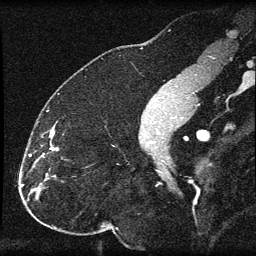
Breast MRI (dynamic contrast-enhanced), one sagittal slice. Dynamic contrast-enhanced series, image 2 of 3 at this slice position (ordered by acquisition). 1.5 T. TE 4.2 ms, TR 8.2 ms. 2 mm slice thickness. 256 × 256 image matrix, field of view 180 × 180 mm. Patient: female, 32 years.
Annotated regions visible in this slice (semi-automatic segmentation, software-assisted and operator-edited):
- analysis volume of interest (the breast-tissue region the enhancement analysis was run in; not a lesion): bounding box [x1, y1, x2, y2] px = [31, 129, 58, 184]
- tumour enhancement mask (voxels above the 70 % enhancement threshold inside the analysis volume of interest): [51, 132, 58, 151]